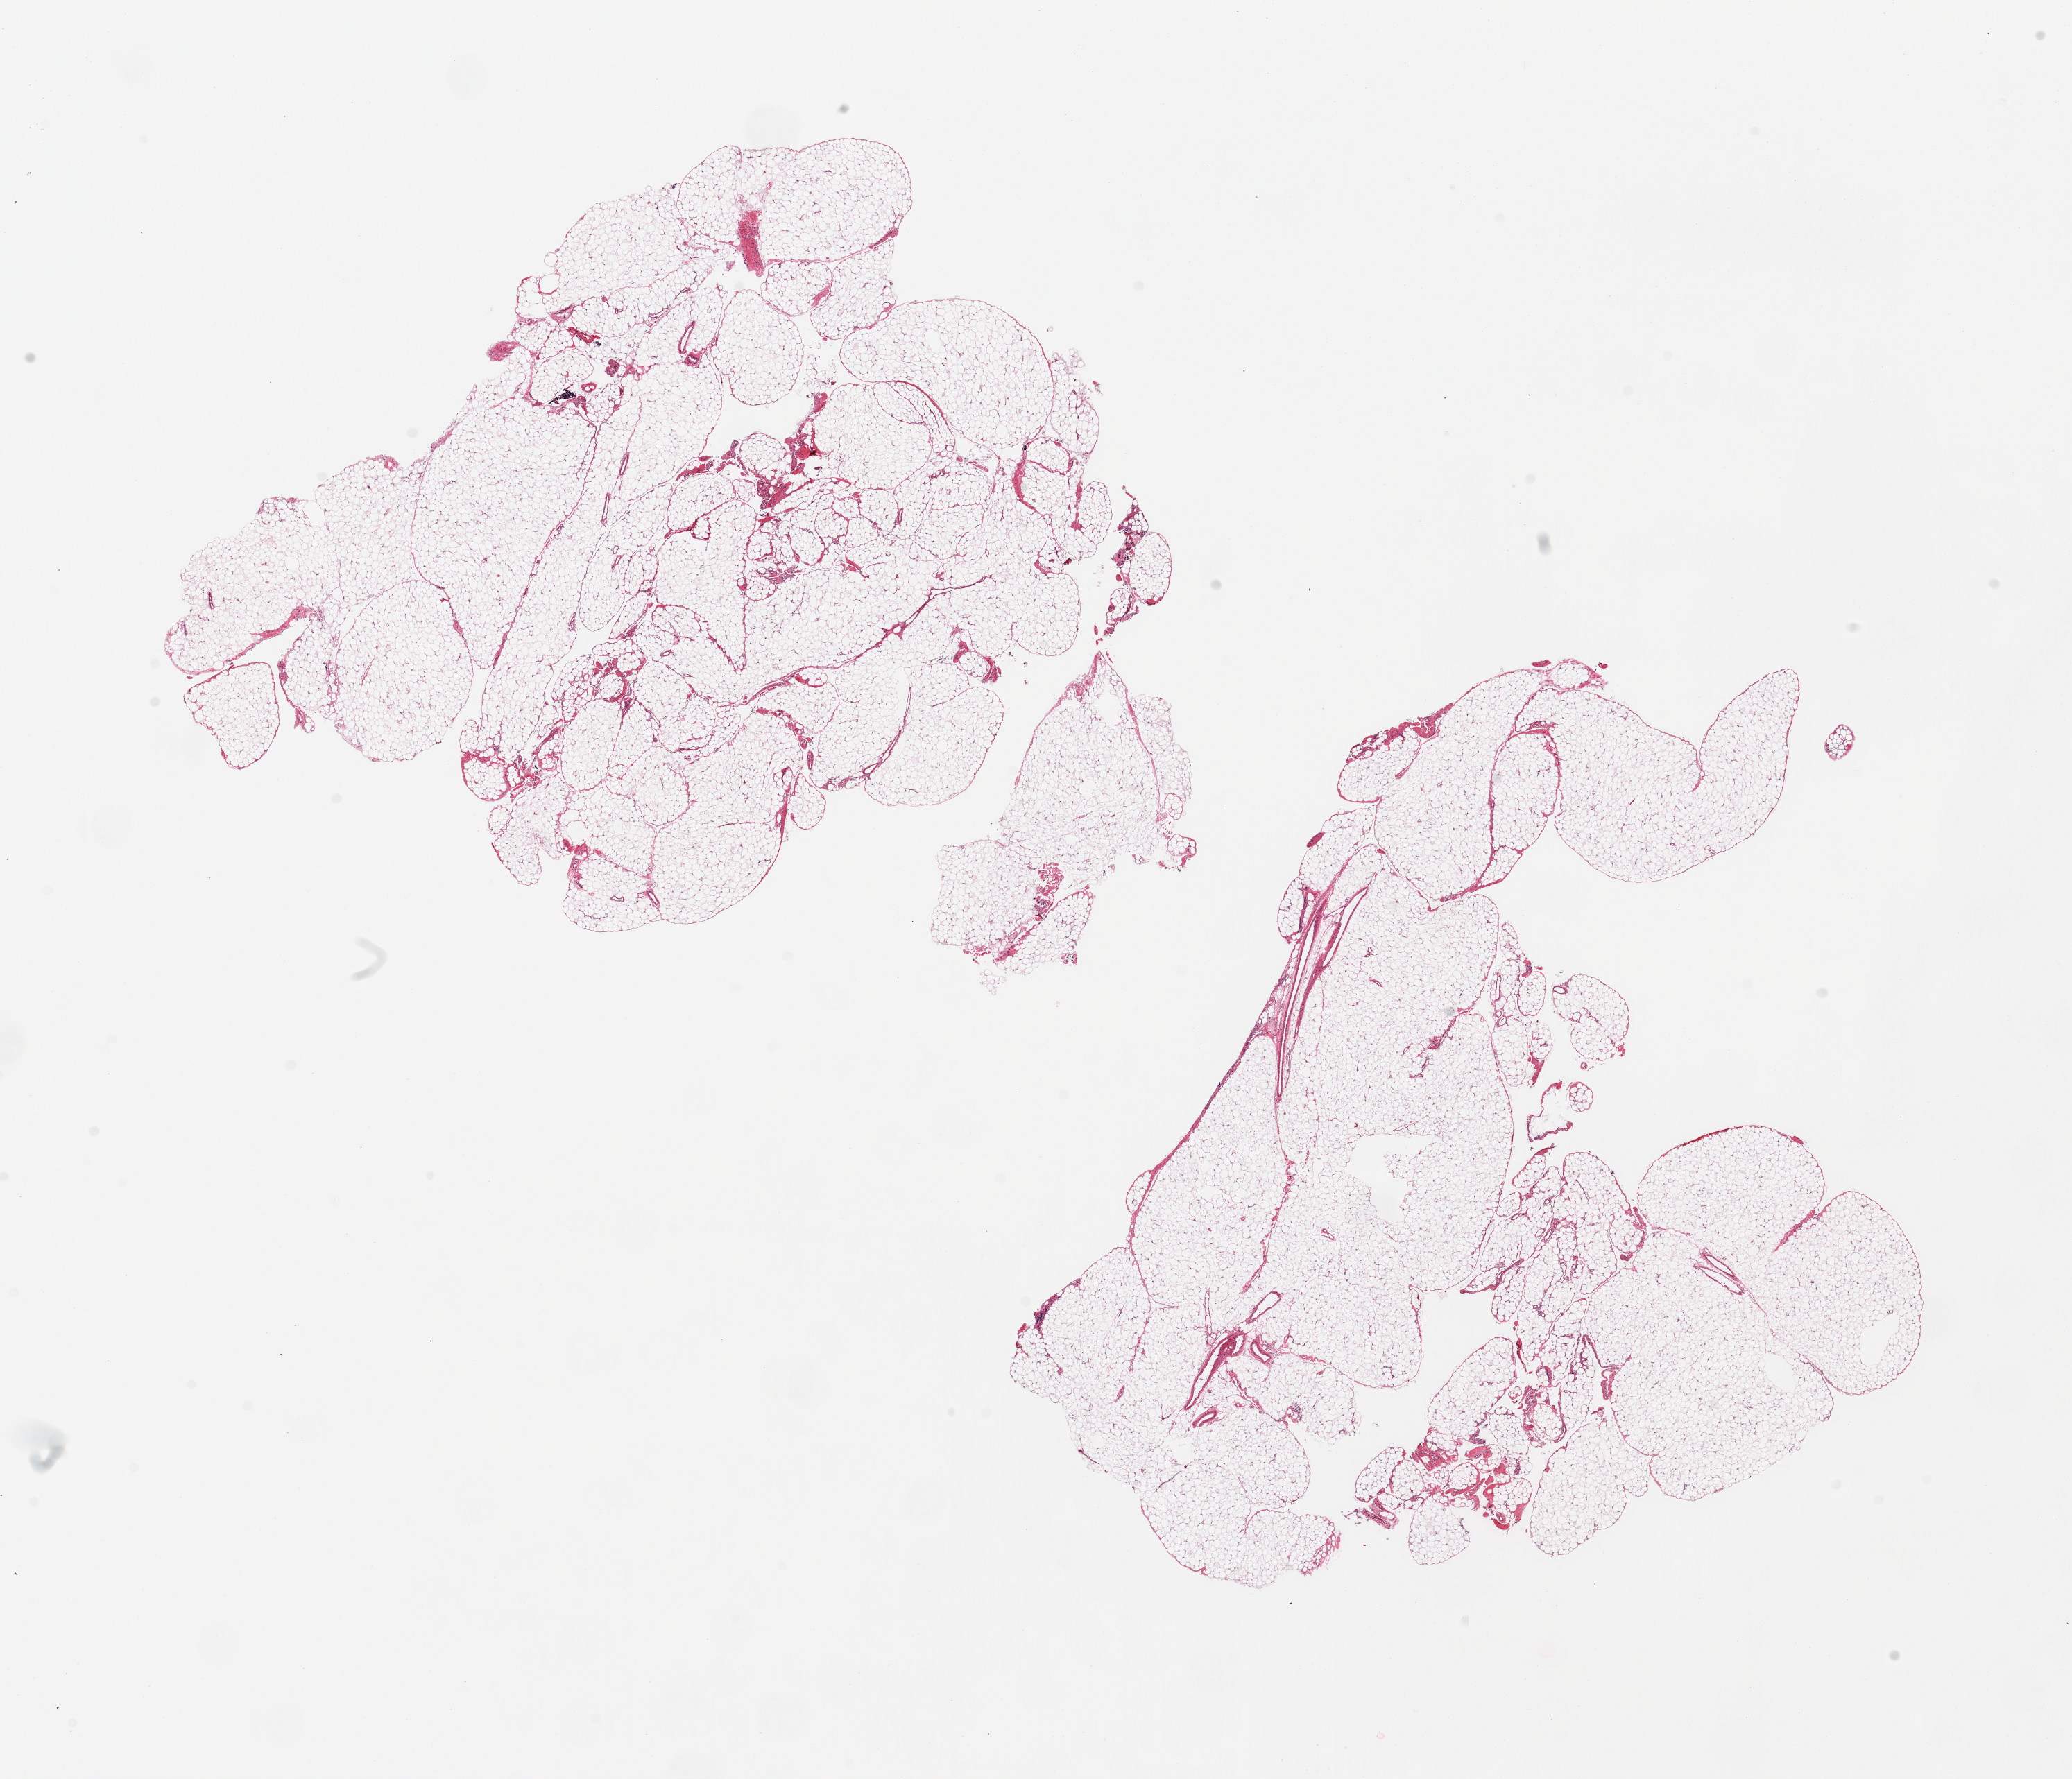
Digitized H&E-stained section, whole scanned area (about 23.6 x 20.3 mm) shown as a low-resolution overview; PAXgene-fixed, paraffin-embedded tissue; sampled site (target tissue): omentum; donor tissue sample.
Review note (as recorded): 2 pieces.